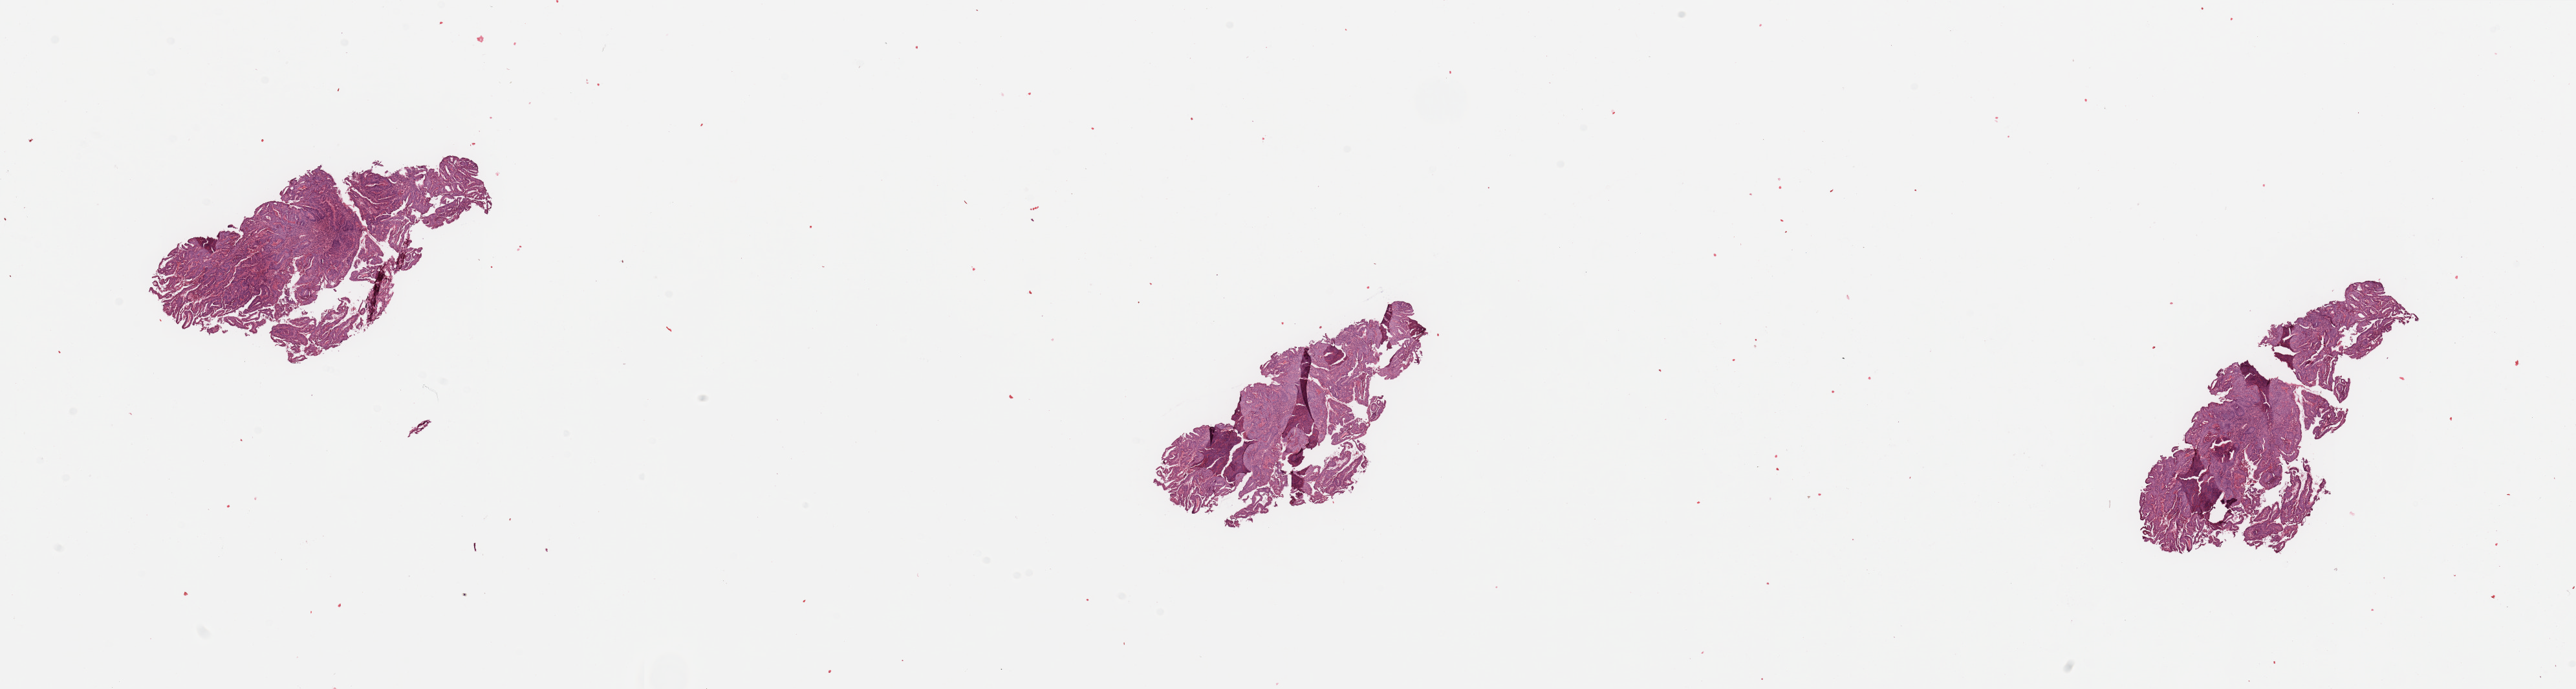
Whole-slide histology image, H&E-stained, low-resolution overview of the scanned area, about 31.5 x 8.4 mm; tumour tissue sample, sampled site: uterus. Female, 77 y/o. Histologic grade: G2 (moderately differentiated). Slide review estimates, as recorded: tumour nuclei 85%, necrosis 2%.
* diagnosis: Endometrioid adenocarcinoma, NOS
* primary tumour site (as recorded): anterior endometrium
* AJCC pathologic stage: I